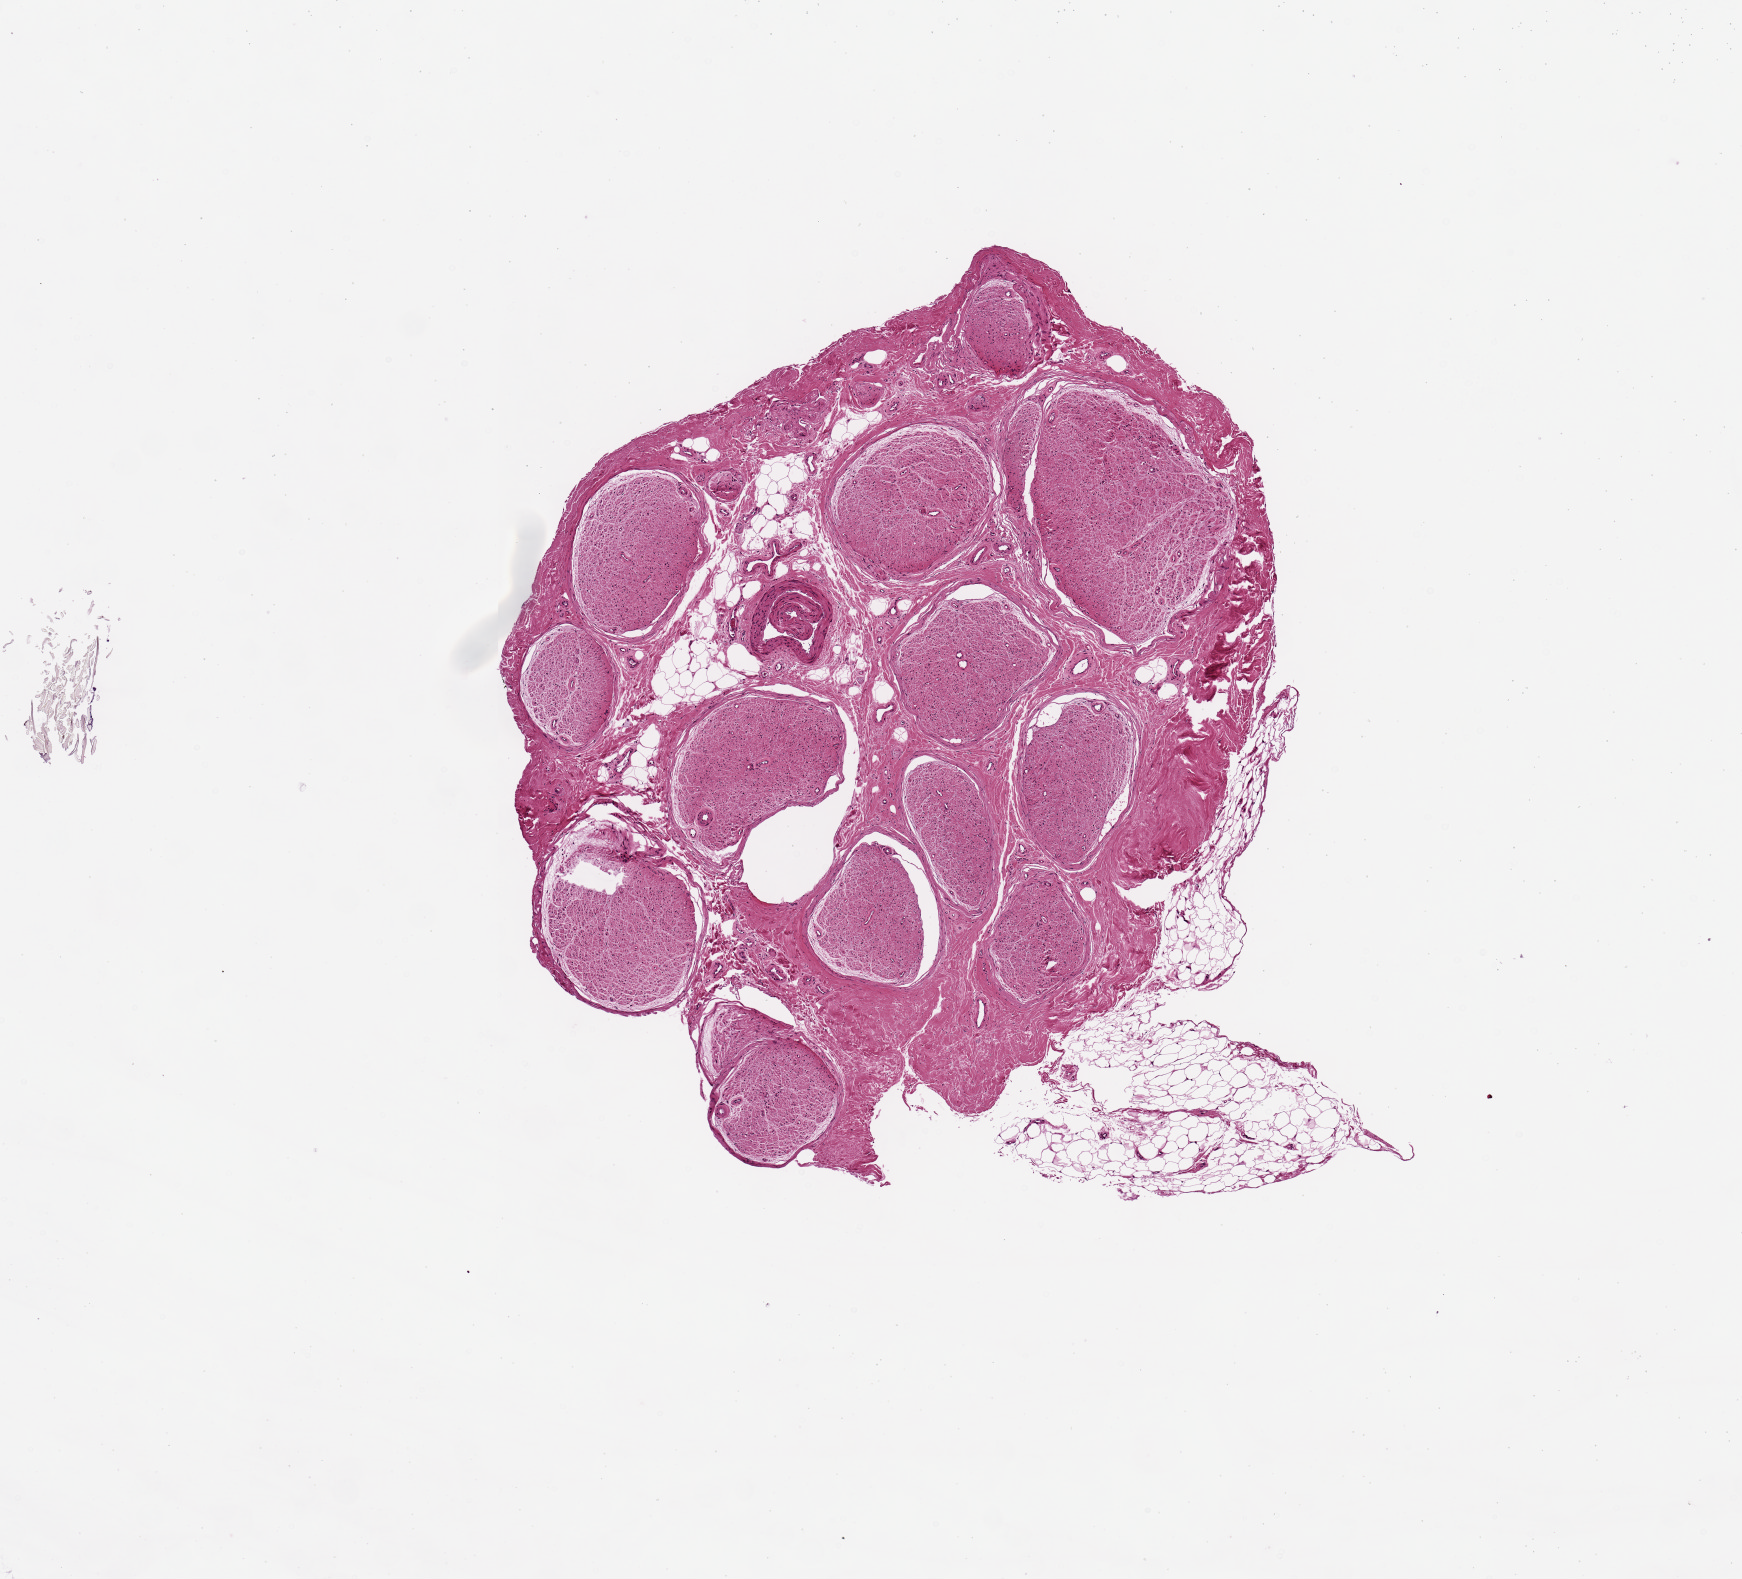
Digitized hematoxylin and eosin (H&E)-stained section, whole scanned area (about 6.9 x 6.2 mm, from a 20x scan) shown as a low-resolution overview, PAXgene-fixed, paraffin-embedded tissue, section of tibial nerve (target tissue), donor tissue sample. Donor: male.
Review note (as recorded): 13 nerve bundles; 20% fat. 3.7x3mm.